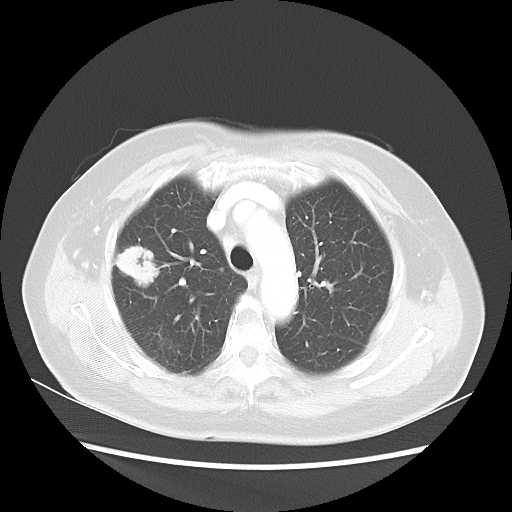
Chest CT, one axial slice; slice 35 of 48 in the series (ordered by position); reconstruction kernel LUNG; lung window (W 1500 / L -600 HU); 5 mm slice thickness; 512 × 512 image matrix. Female patient, age 75 years. From the clinical record (not read from this slice): clinical TNM (as recorded): T1c N0 M0.
Outlined on this slice (bounding box drawn by a radiologist):
- lung tumour (recorded histology: adenocarcinoma): bounding box [x1, y1, x2, y2] px = [115, 239, 167, 292]